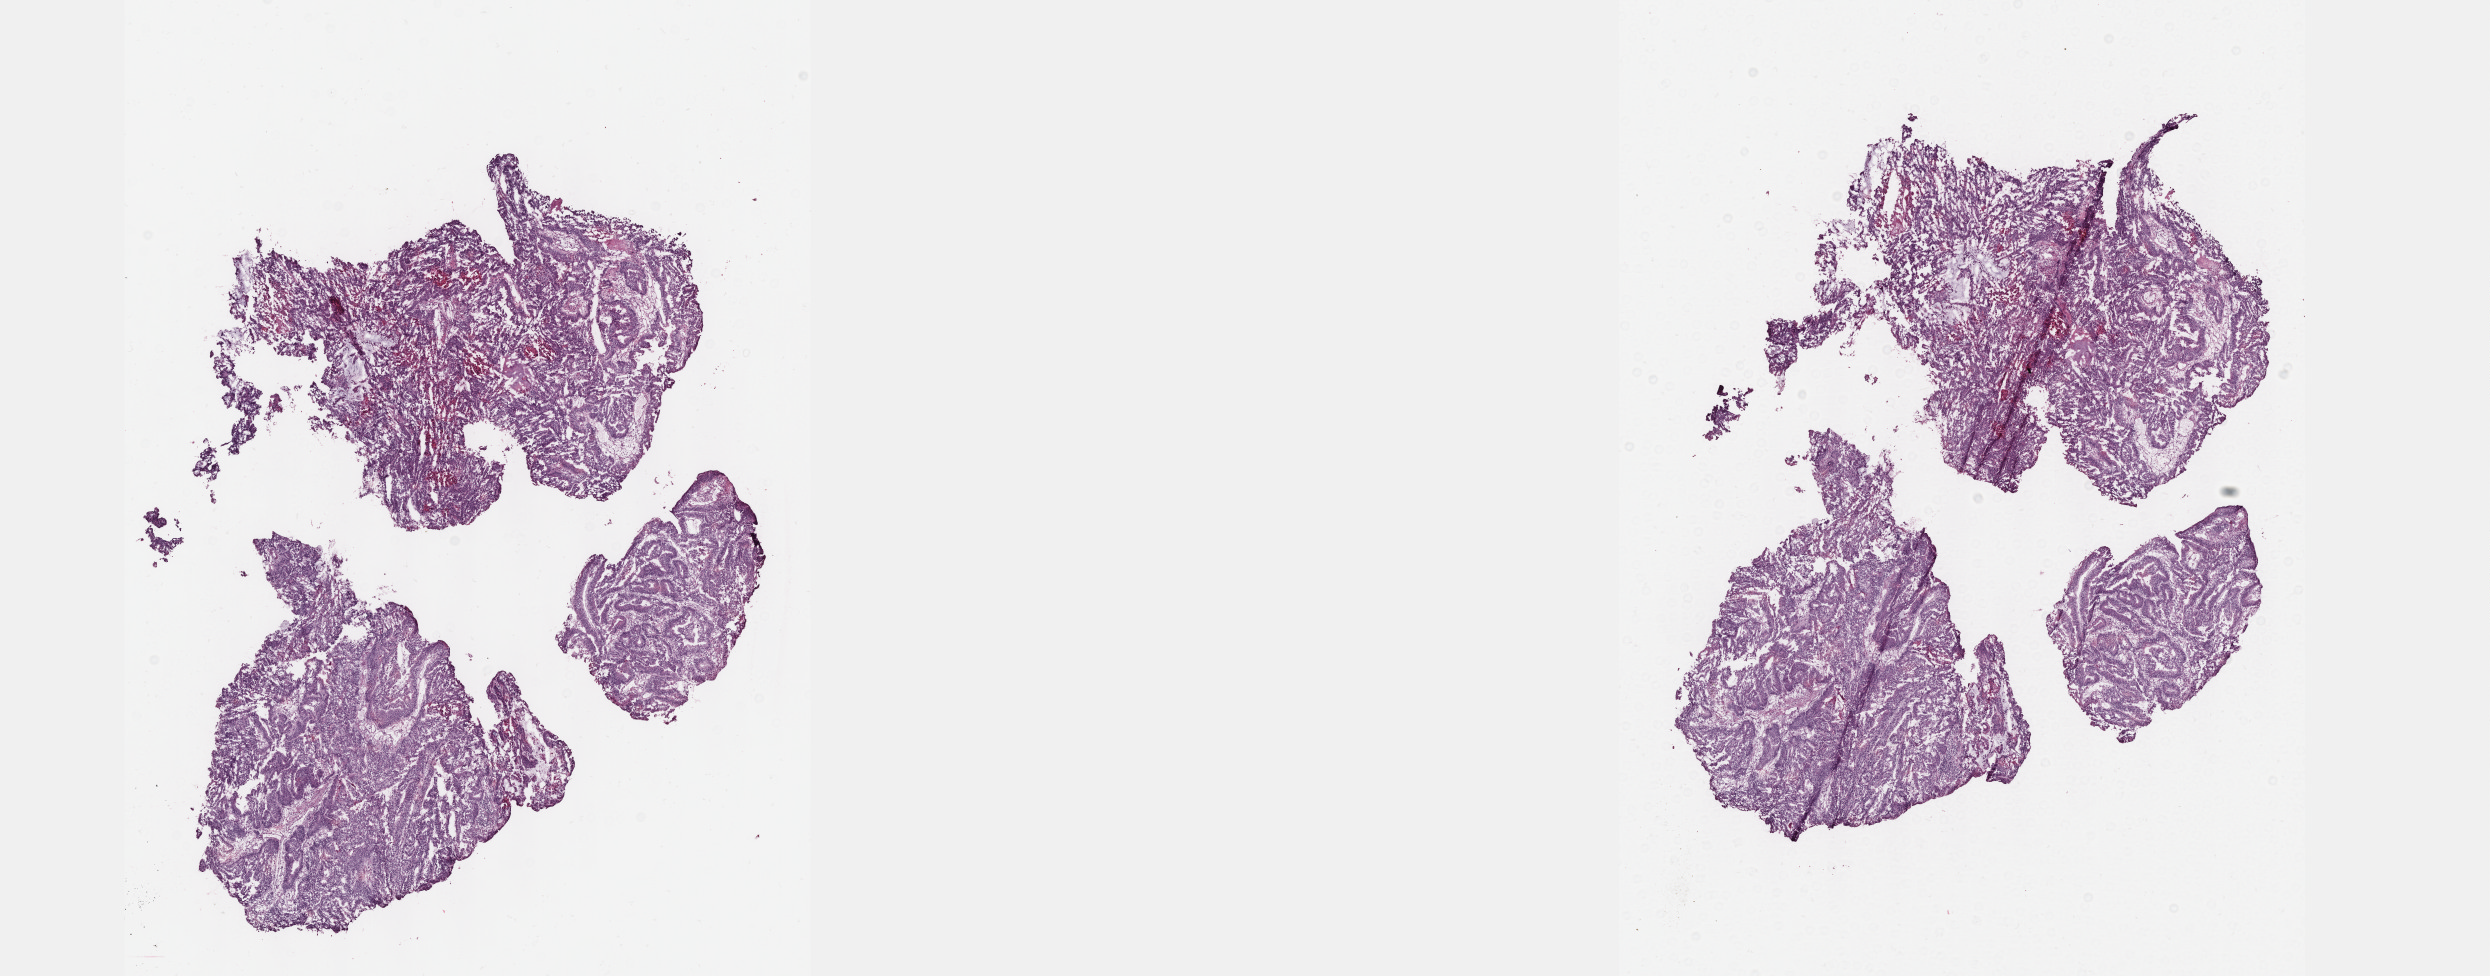
H&E whole-slide image — low-resolution overview of the scanned area, about 20.1 x 7.9 mm (from a 40x scan), frozen section from the top of the tissue portion, colon, primary tumour sample. Female, age 70 years at initial diagnosis. Composition of this section per pathologist review: tumour cells 94%, tumour nuclei 90%, normal cells 0%, stromal cells 5%, necrosis 1%. Inflammatory infiltration, as recorded: lymphocyte infiltration 2%, monocyte infiltration 1%, neutrophil infiltration 0%.
AJCC pathologic stage: IV (6th edition). Lymph nodes positive (case pathology): 0 of 13 examined. Diagnosis: Adenocarcinoma, NOS. TNM: T3 N0 M1.